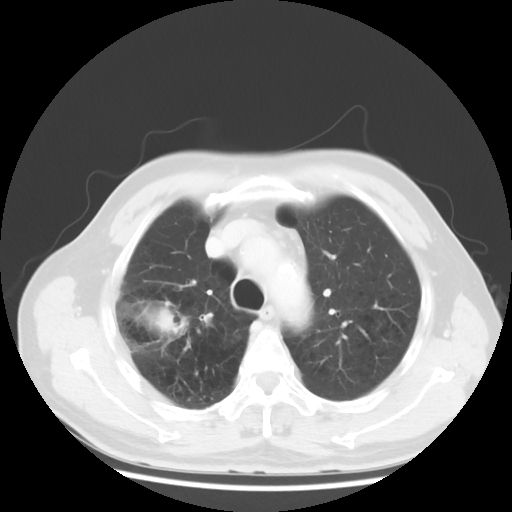
Chest CT, one axial slice; position 38 of 50 along the scan axis; reconstruction kernel STANDARD; lung window (W 1500 / L -600 HU); 5 mm slice thickness; 512 × 512 image matrix. Patient: male, 69 years. From the clinical record (not read from this slice): clinical TNM (as recorded): T3 N0 M0; histopathological grade: G3.
Annotated regions visible in this slice (rectangle marked by the reading radiologist):
- lung tumour (recorded histology: adenocarcinoma): bounding box [x1, y1, x2, y2] px = [115, 293, 194, 355]